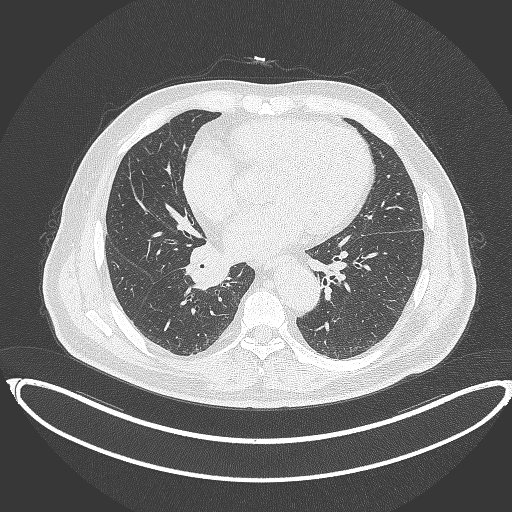
Chest CT, one axial slice; slice 180 of 387 in the series (ordered by position); 120 kVp; lung window (W 1500 / L -600 HU); 1 mm slice thickness; 512 × 512 image matrix, field of view 448 × 448 mm. Male patient, age 61 years. Case-level facts recorded for this patient, not image findings: clinical TNM (as recorded): T1b N1 M0.
Outlined on this slice (bounding box drawn by a radiologist):
- lung tumour (recorded histology: squamous cell carcinoma): box from (x=180, y=240) to (x=231, y=293) px